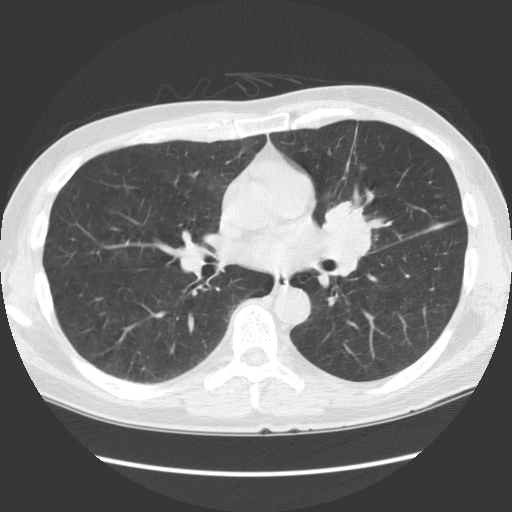
Axial slice from a low-dose chest CT screening exam; baseline annual screen; lung window (W 1500 / L -600 HU); 2.5 mm slice thickness; slice 70 of 136 in the series. Male, age 61 years at enrolment. Former smoker at enrolment.
Expert-annotated lung lesion, bounding box [x1, y1, x2, y2] px = [296, 191, 393, 292]. Reader record for this screening exam (exam-level; its link to the box is not recorded): non-calcified nodule or mass ≥4 mm, lingula, 35 × 35 mm, spiculated (stellate) margins, soft tissue attenuation. Official screen result: positive, change unspecified: nodule(s) >= 4 mm or enlarging nodule(s), mass(es), or other non-specific abnormalities suspicious for lung cancer. Lung cancer was diagnosed 58 days after this screen: squamous cell carcinoma, NOS, left hilum, left main stem bronchus, poorly differentiated (G3), stage IA (AJCC 6th edition), 40 mm at pathology.